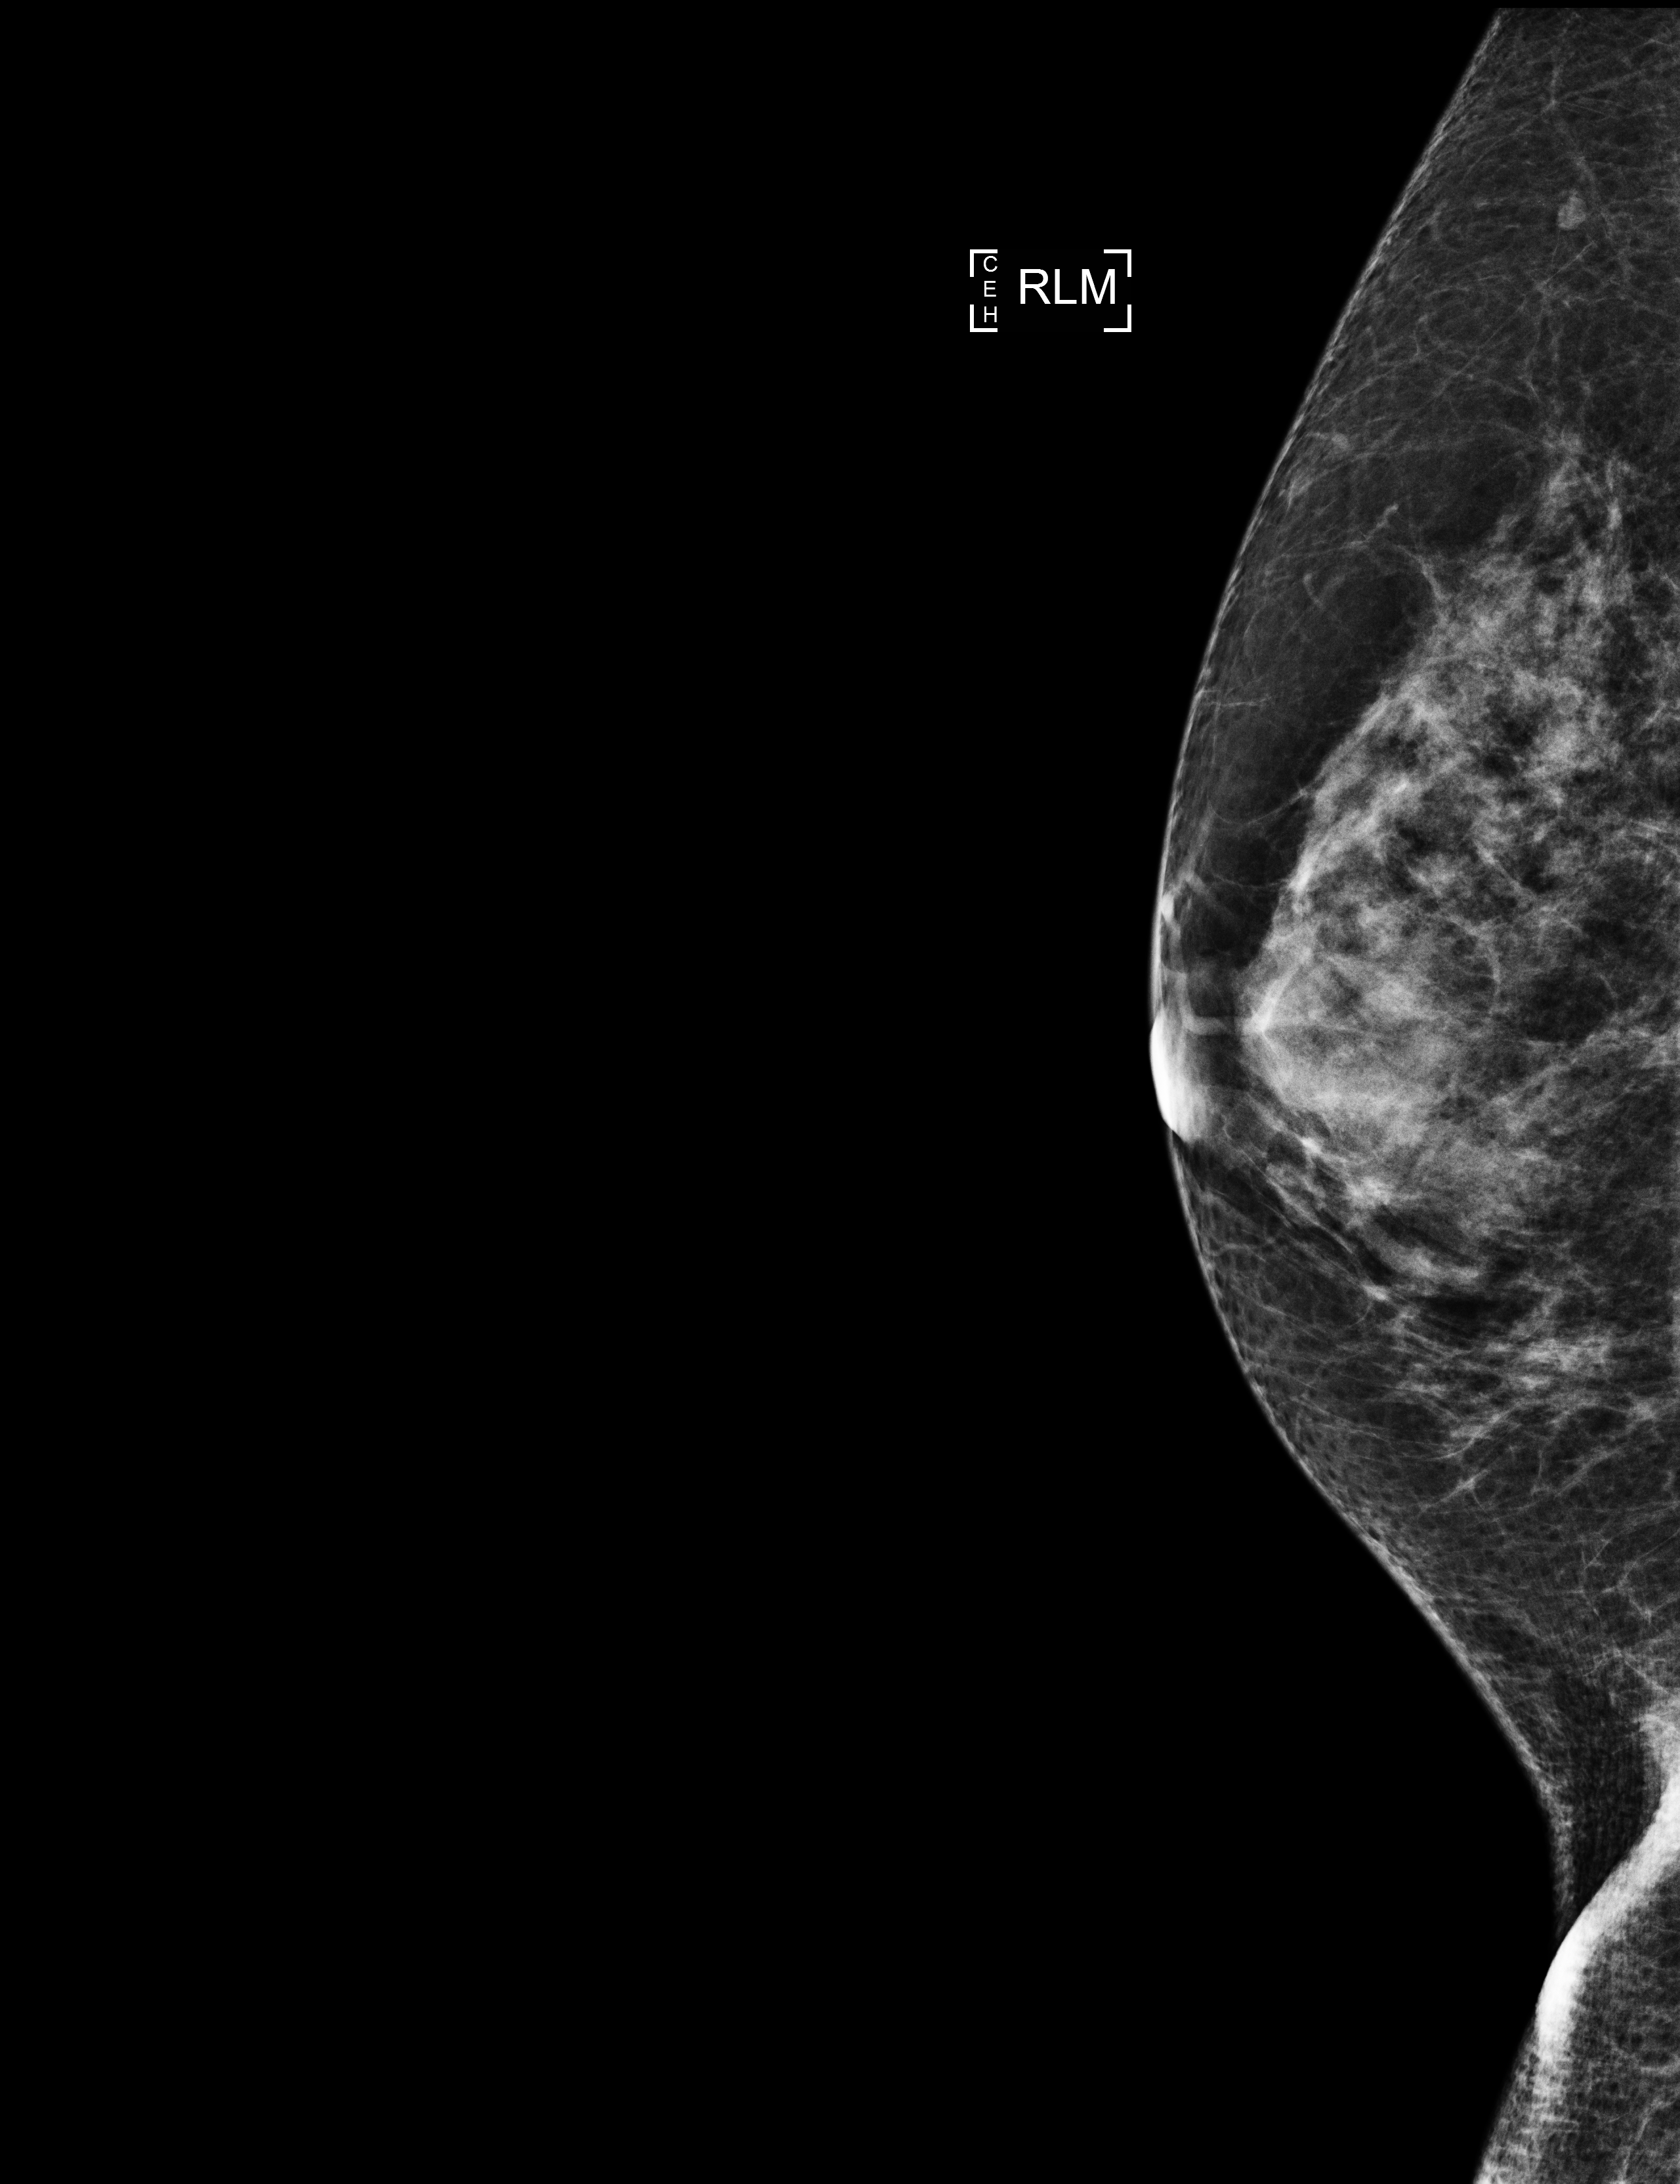
Annual screening mammography examination. Female patient, age 60 years.
Image type: full-field digital mammogram. Breast: right. Projection: lateromedial (LM) view.